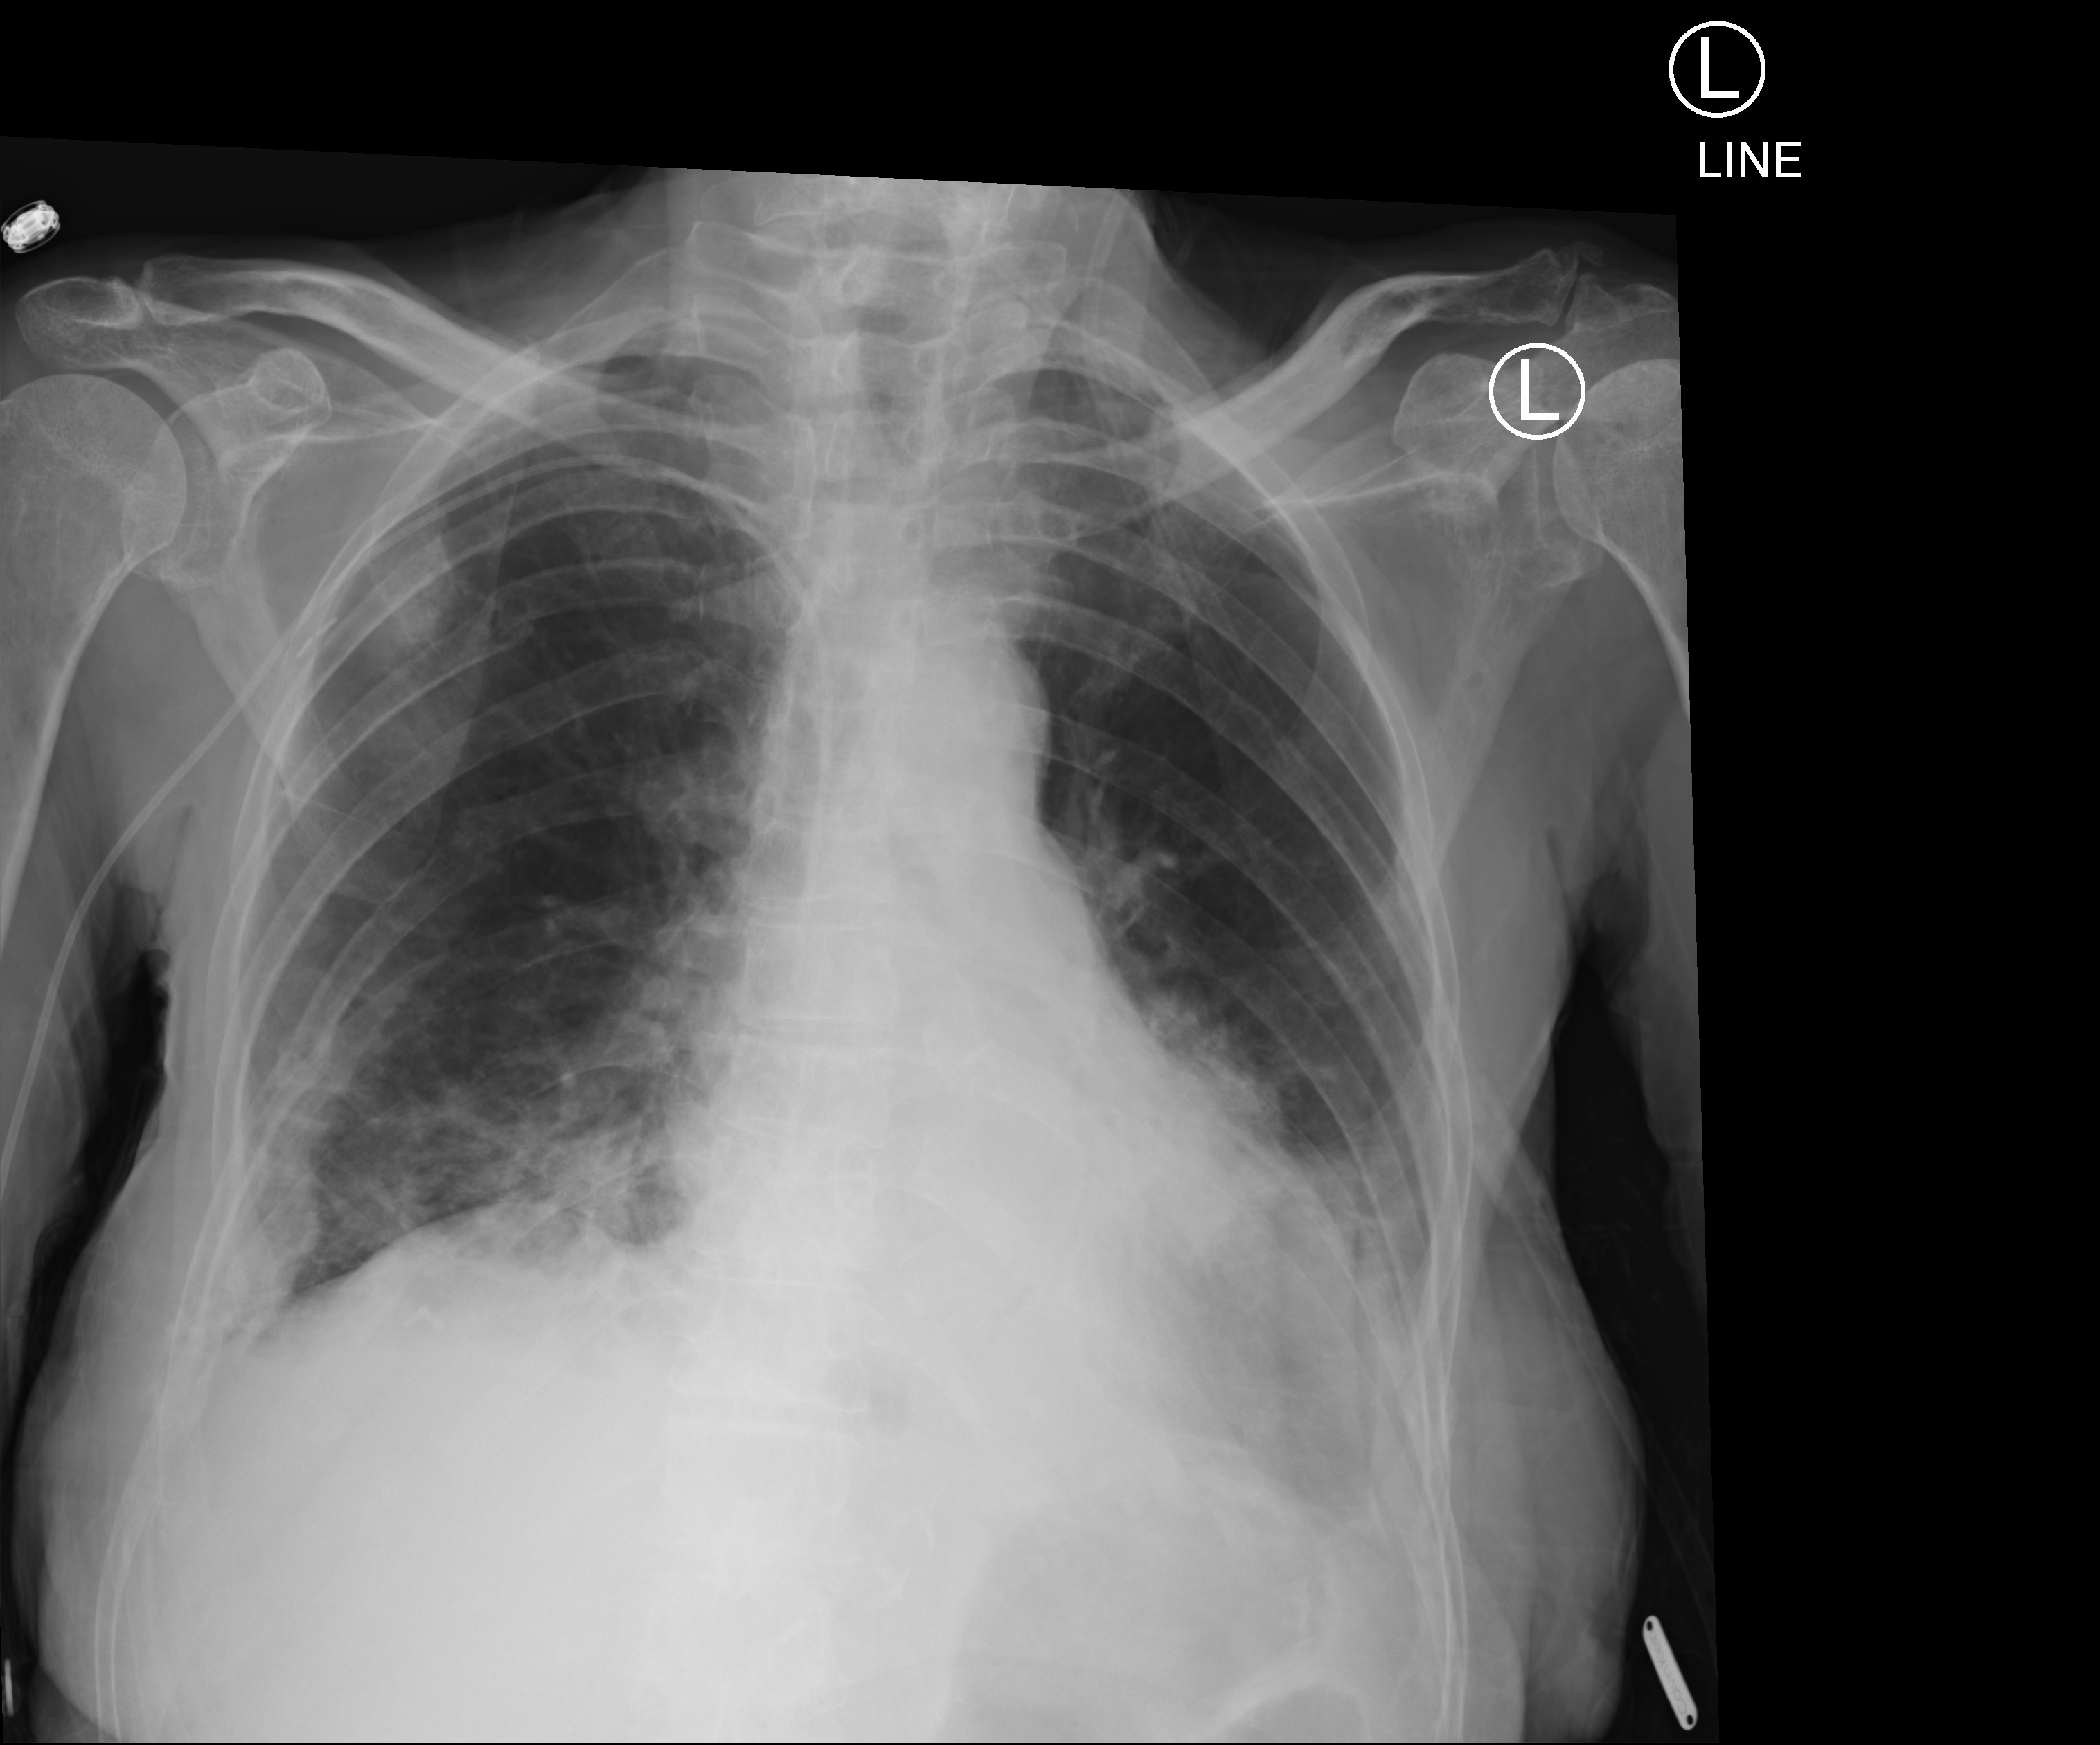
Bedside chest radiograph (computed radiography). Patient hospitalised with COVID-19; female, aged 60–74 years.
From the hospital-stay record, not from the radiograph (when in the stay this image was taken is not recorded): admitted to intensive care during this hospital stay: no.